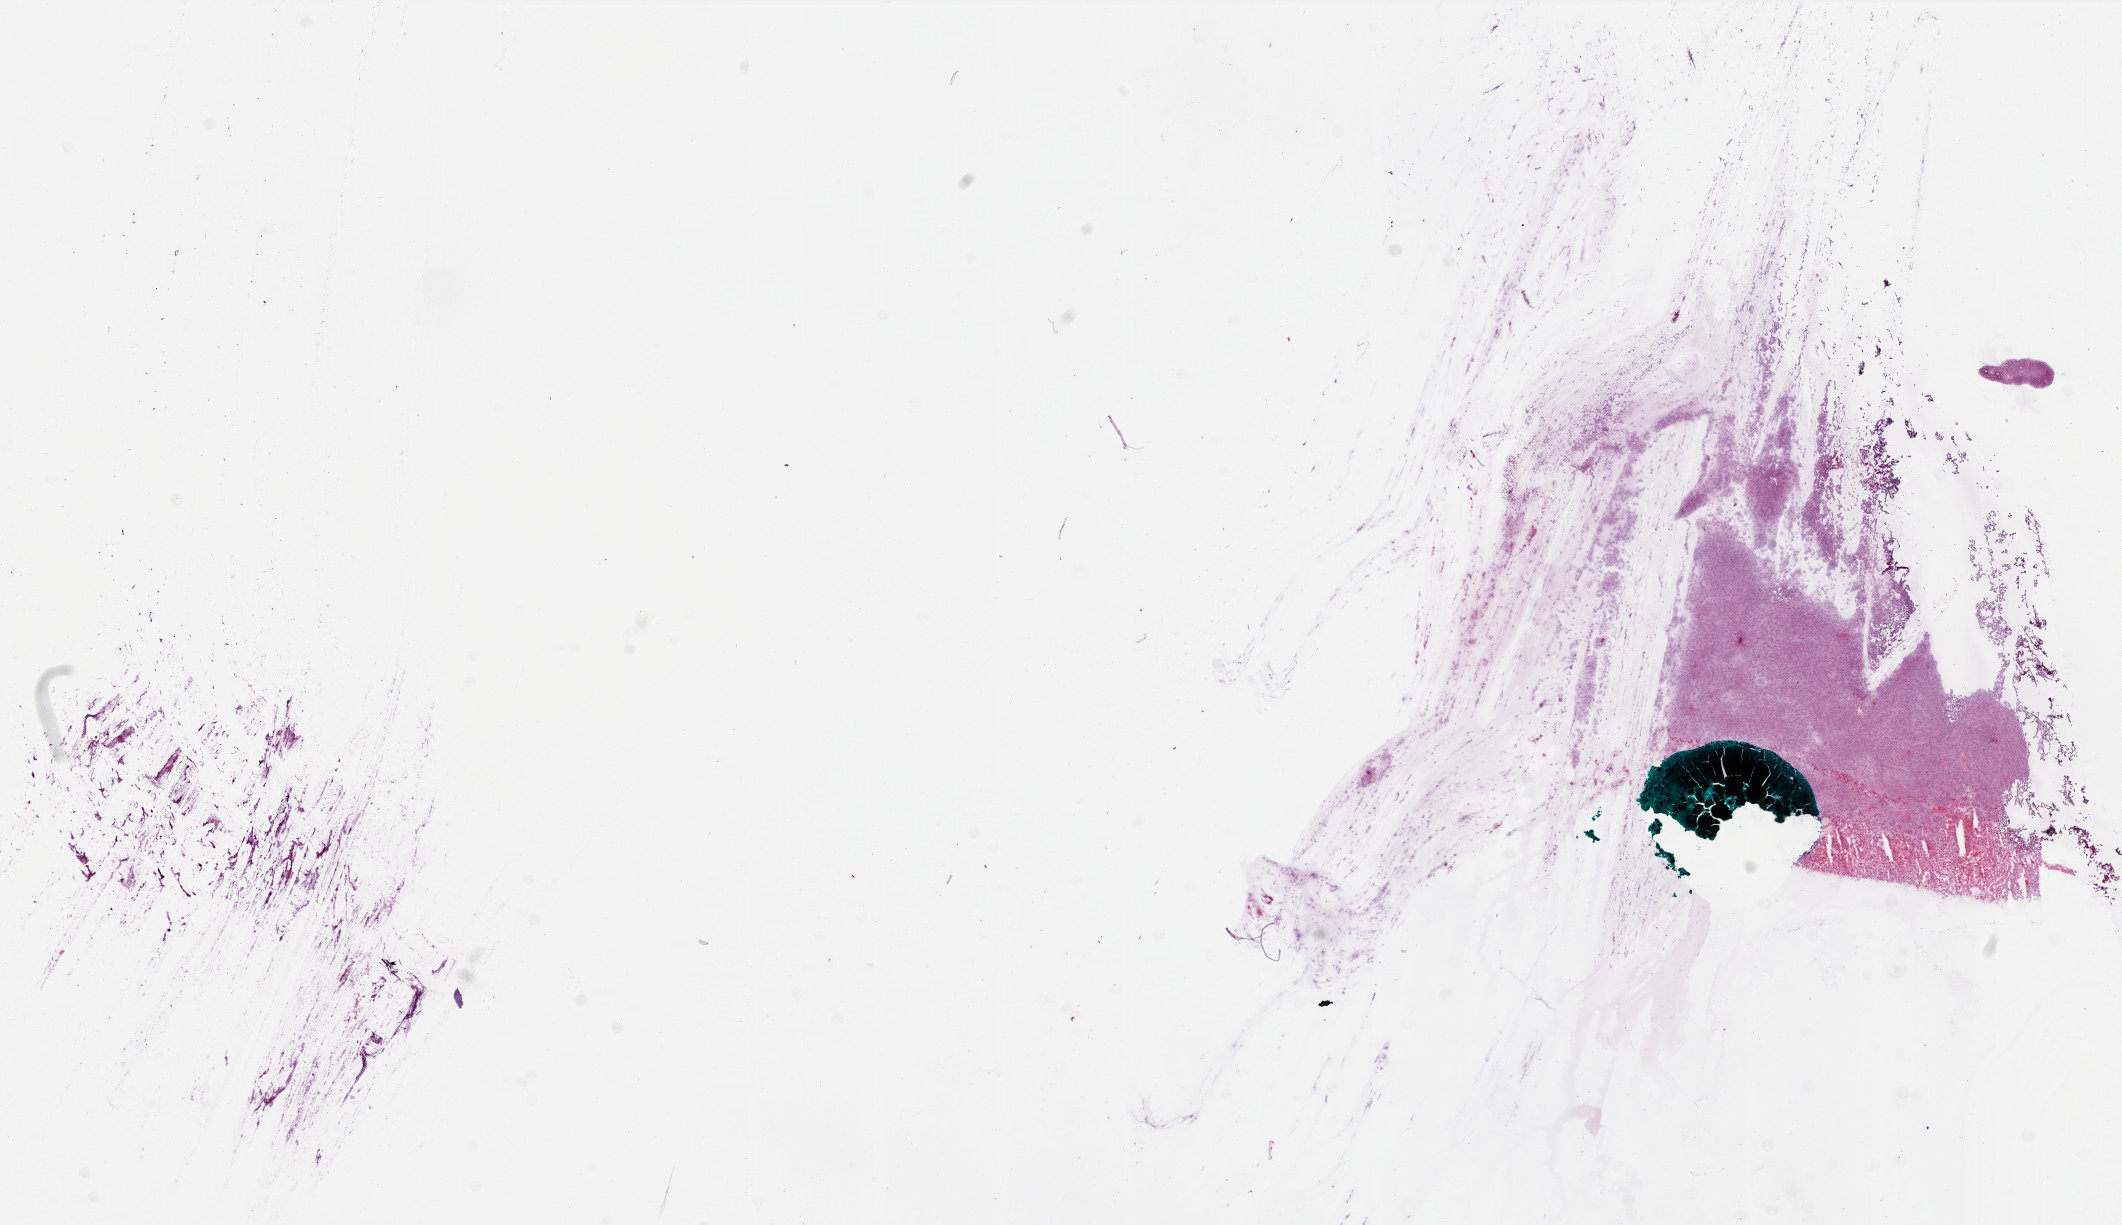
H&E whole-slide image — low-resolution overview of the scanned area, about 17.0 x 9.8 mm (from a 20x scan), frozen section, primary tumour sample from the brain. Patient: female, age at initial diagnosis 51 years. Composition of this section per pathologist review: tumour cells 85%, tumour nuclei 100%.
Pathologic diagnosis: Glioblastoma.